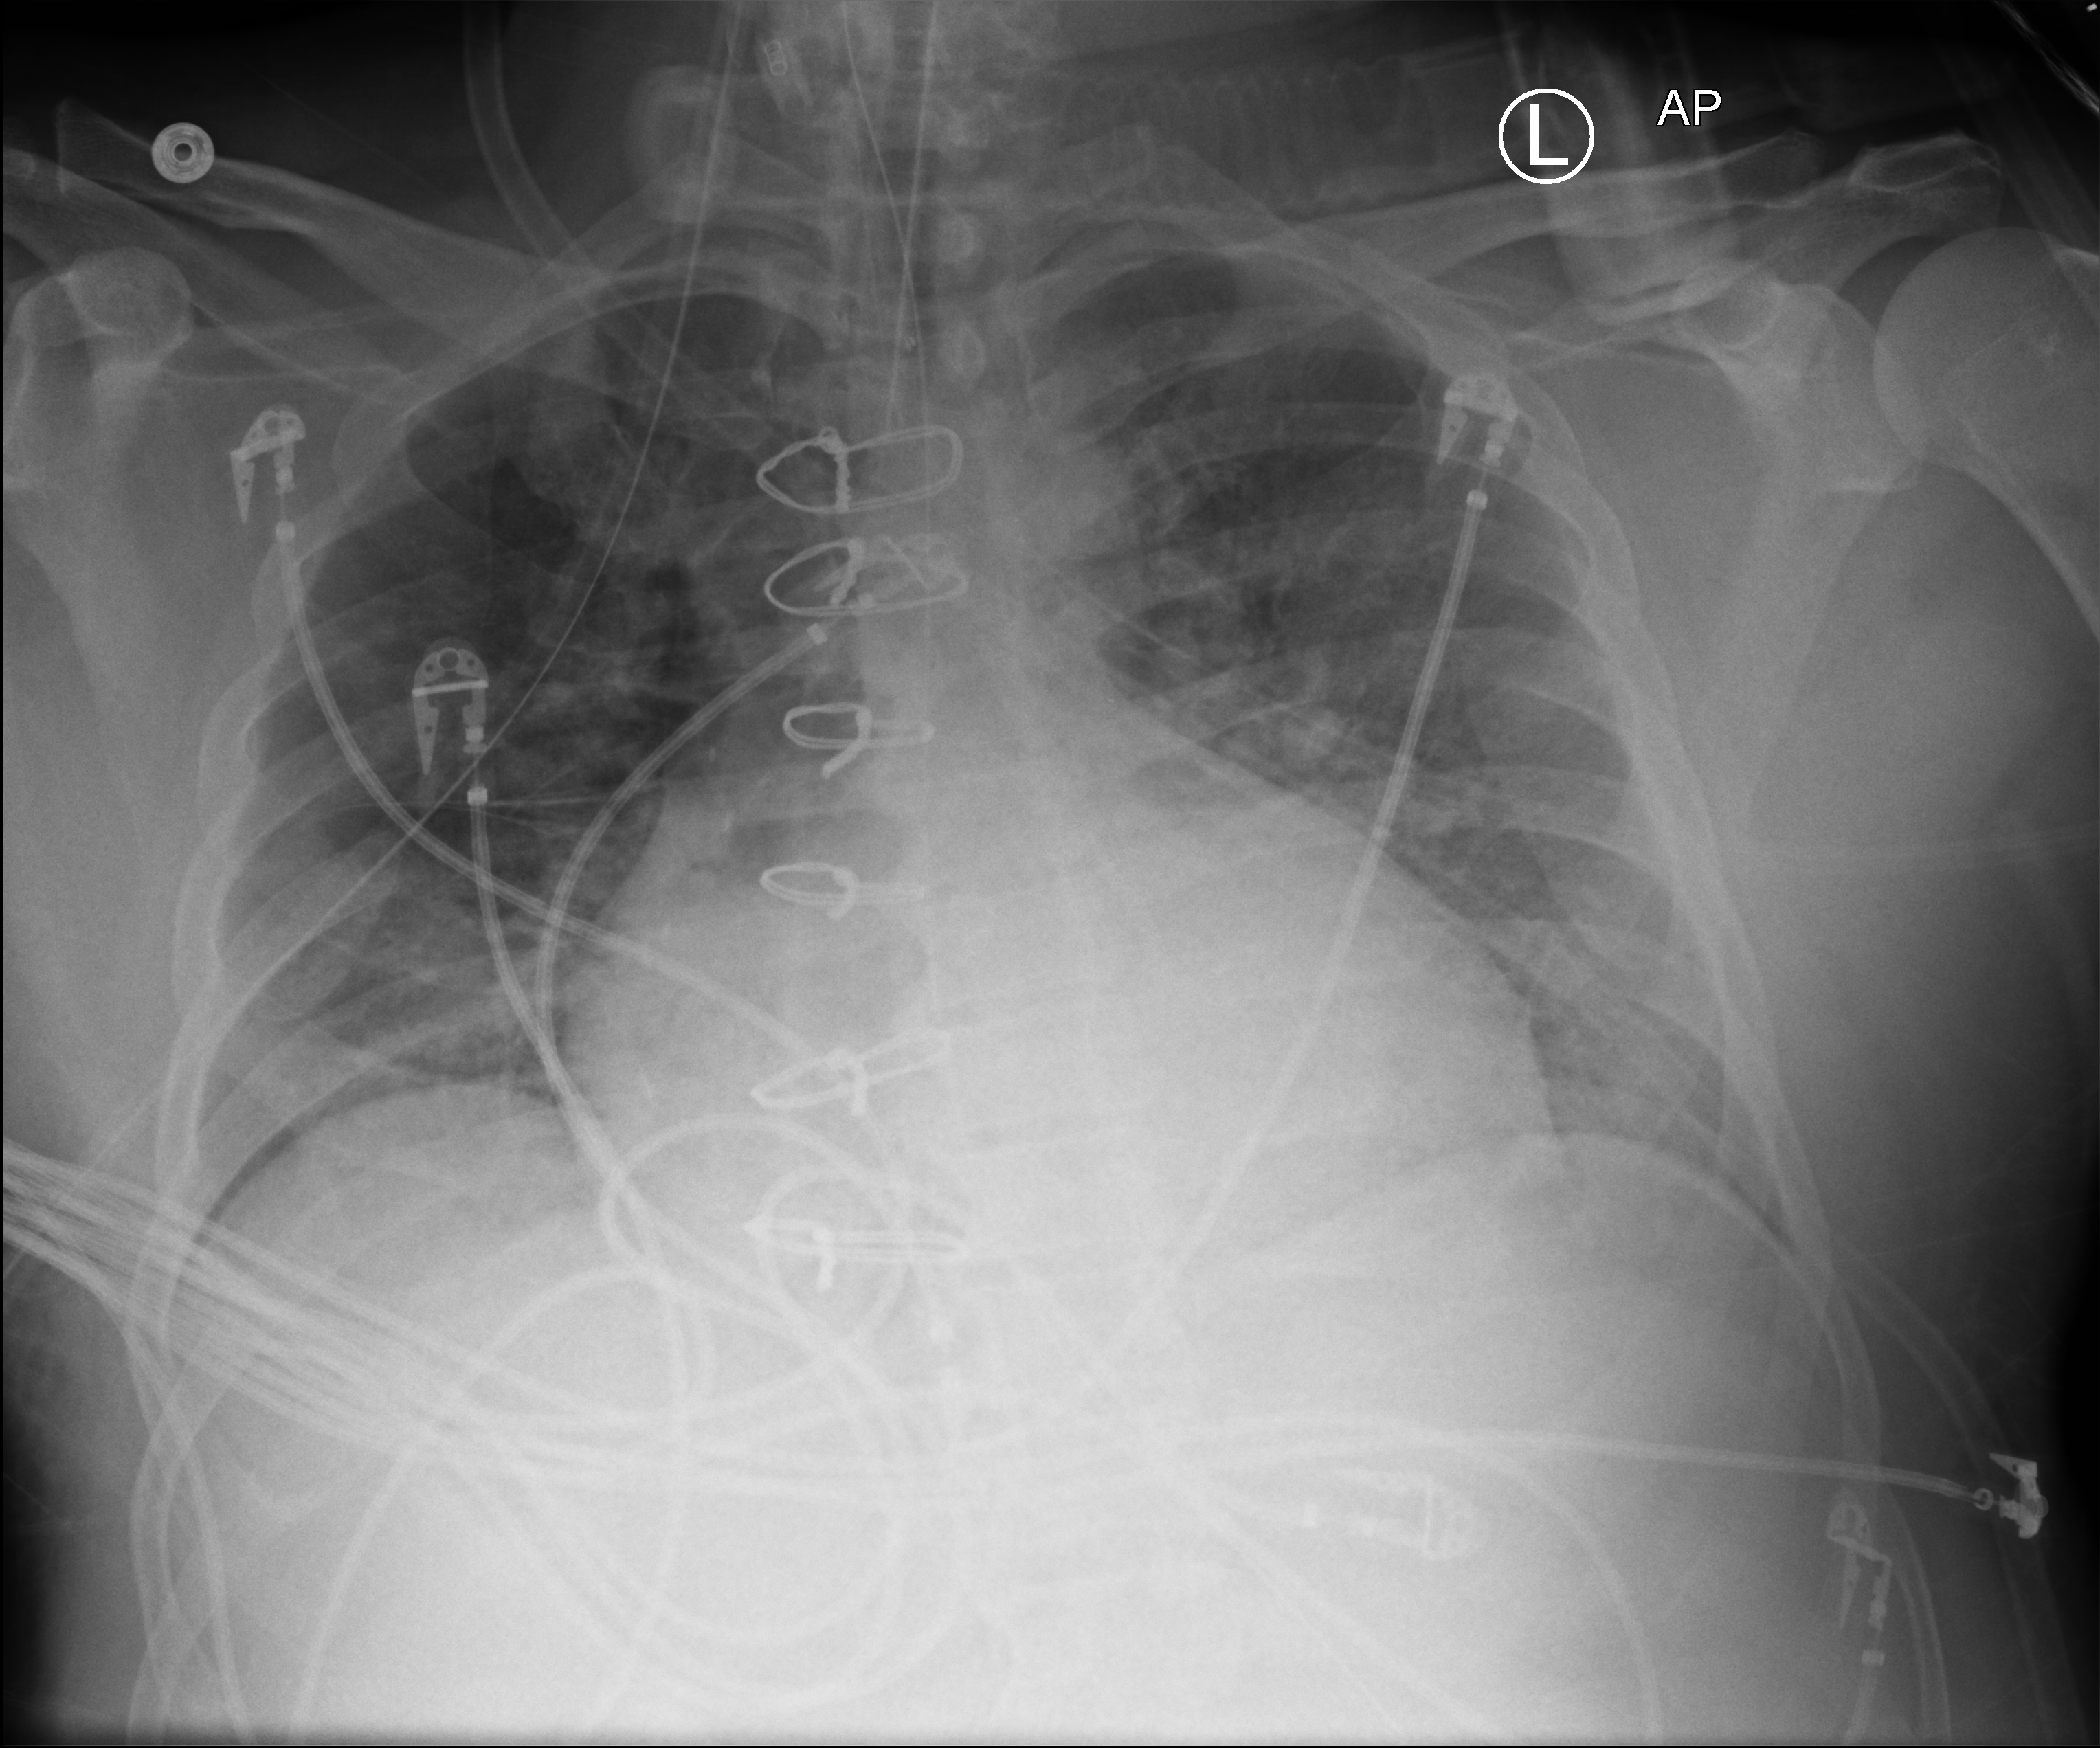
Bedside chest radiograph (computed radiography); anteroposterior (AP) projection. Adult patient hospitalised with COVID-19, age 18–59 years.
Admission-level facts for this patient (not findings on this image; timing relative to this image not recorded): admitted to intensive care during this hospital stay: yes; mechanically ventilated during this hospital stay: yes.